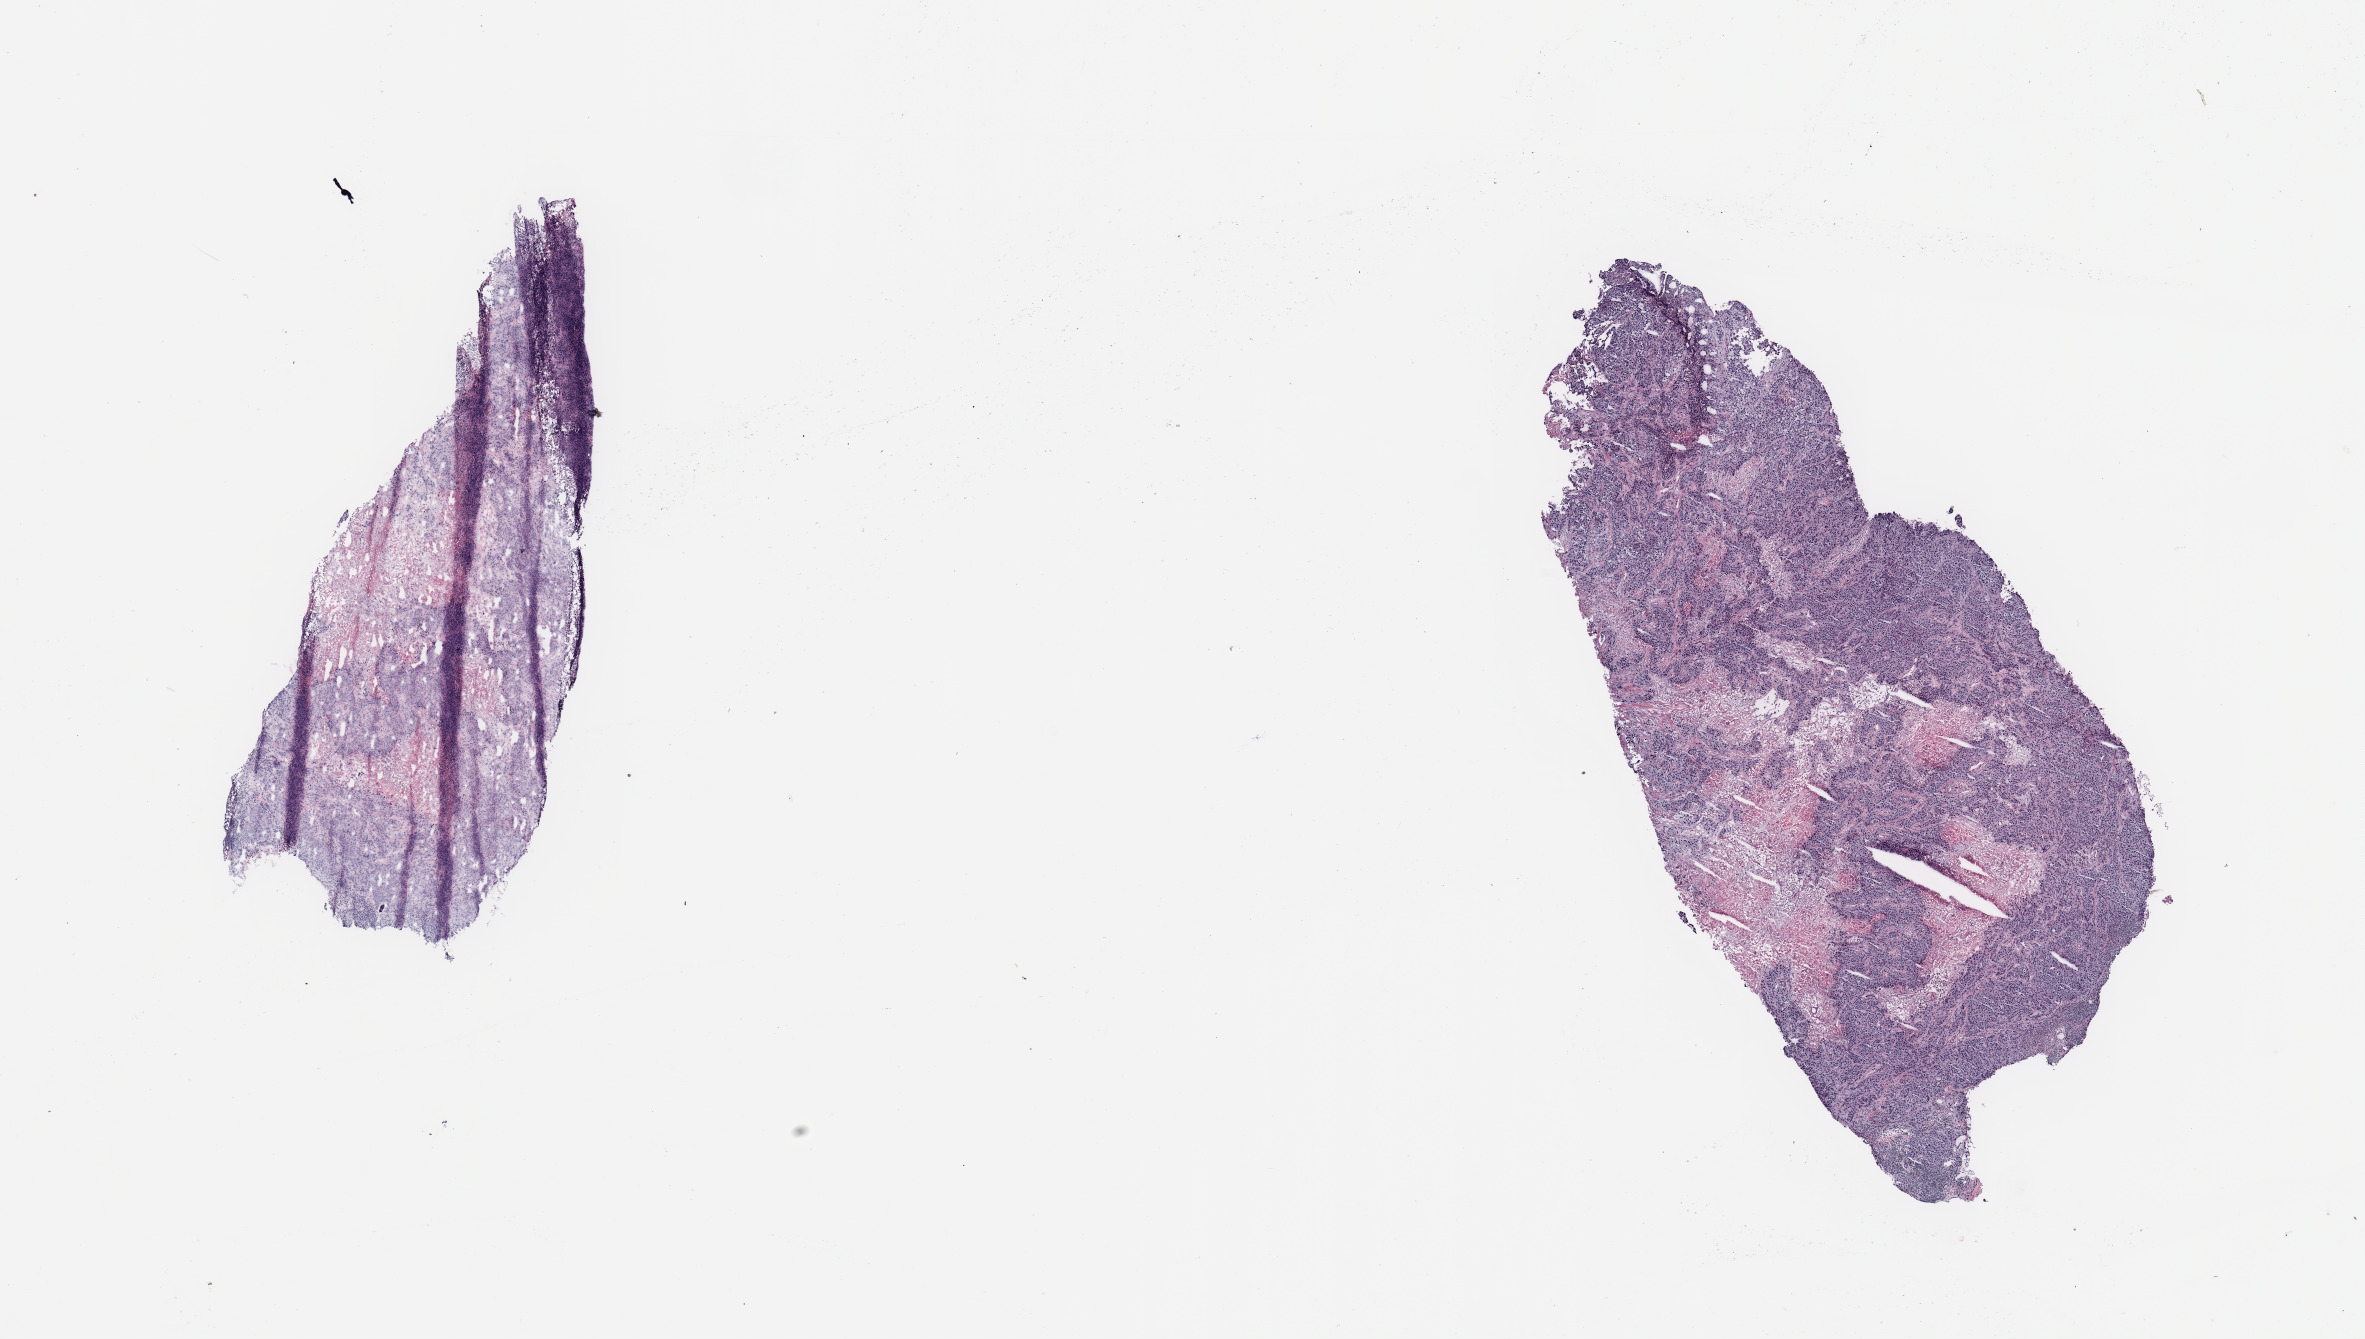
Whole-slide histology image, H&E, whole scanned area (about 18.7 x 10.6 mm) shown as a low-resolution overview; tumour tissue sample, breast. Female, 42 y/o.
- AJCC pathologic stage: IIA
- diagnosis: Infiltrating duct carcinoma, NOS